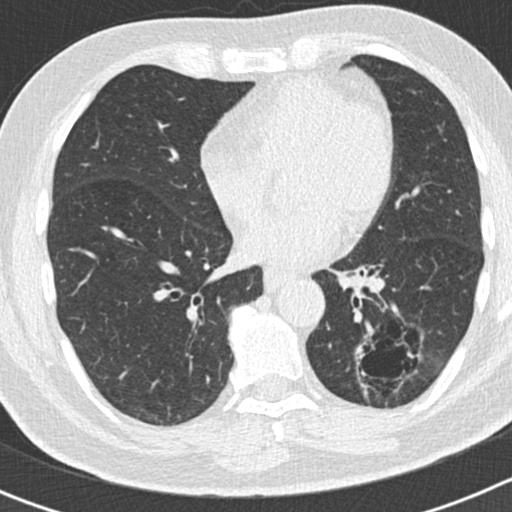
Axial slice from a low-dose chest CT screening exam; second annual screen; lung window (W 1500 / L -600 HU); 2 mm slice thickness; slice 97 of 186 in the series. Male, age 66 years at enrolment.
Expert reader's lesion annotation, bounding box [x1, y1, x2, y2] px = [347, 328, 415, 404]. Reader record for this screening exam (exam-level; its link to the box is not recorded): non-calcified nodule or mass ≥4 mm, left lower lobe, 50 × 33 mm, smooth margins, pre-existing on the prior screen: yes; interval growth: yes. Official screen result: positive, other. Participant outcome: lung cancer diagnosed 440 days after this screen (after the third annual screen) — adenocarcinoma, NOS, left lower lobe, poorly differentiated (G3), stage IB (AJCC 6th edition), 38 mm at pathology.